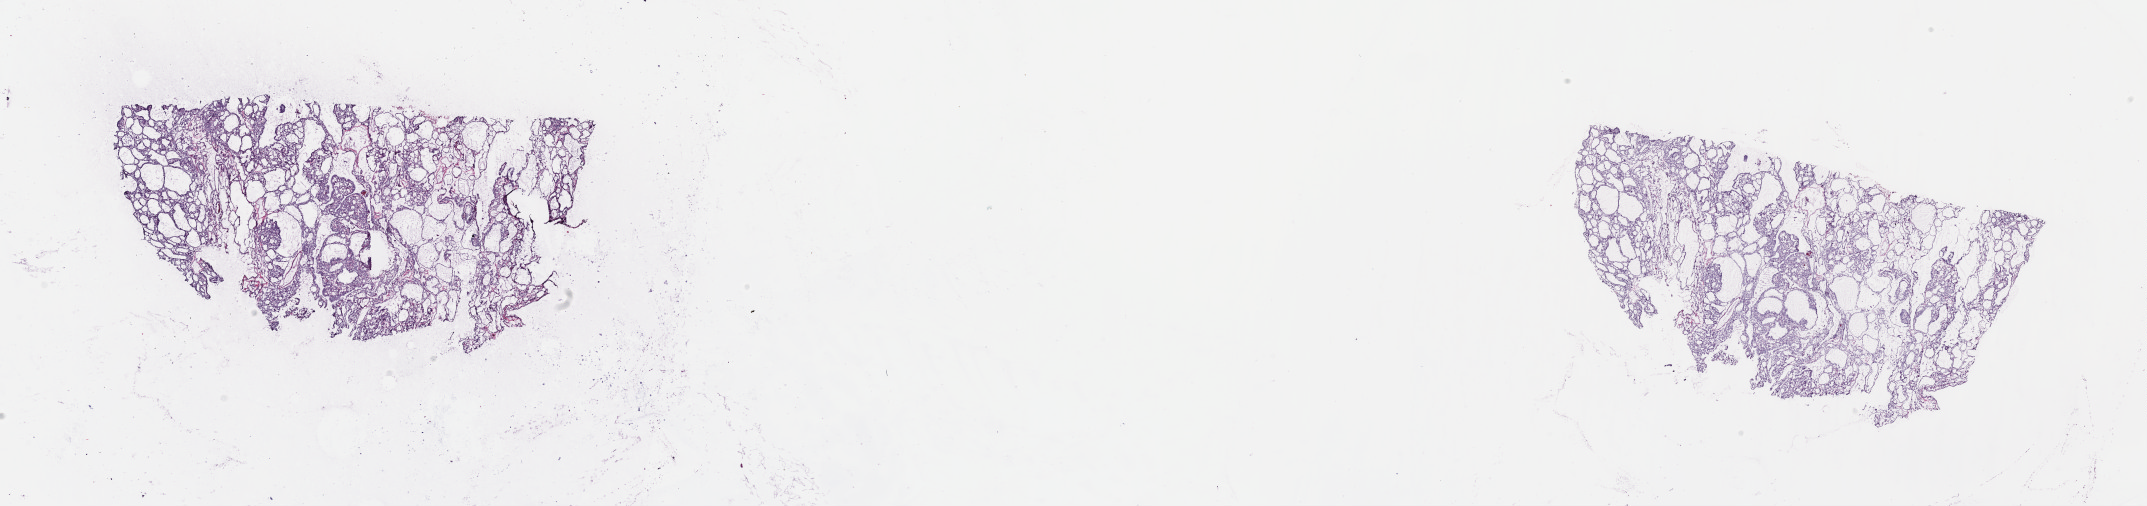
Digitized Hematoxylin and eosin (H&E) stained tissue section (whole slide) — whole scanned area (about 34.7 x 8.2 mm) shown as a low-resolution overview, frozen section from the top of the tissue portion, sample: primary tumour, thyroid. Female patient; age at initial diagnosis 50 years. Slide review estimates, as recorded: tumour cells 95%, tumour nuclei 100%, normal cells 0%, stromal cells 5%, necrosis 0%. Inflammatory infiltration, as recorded: lymphocyte infiltration 0%, monocyte infiltration 1%, neutrophil infiltration 0%.
TNM: T3 N1b MX. AJCC pathologic stage: IVA (7th edition). Diagnosis: Papillary adenocarcinoma, NOS (thyroid gland).